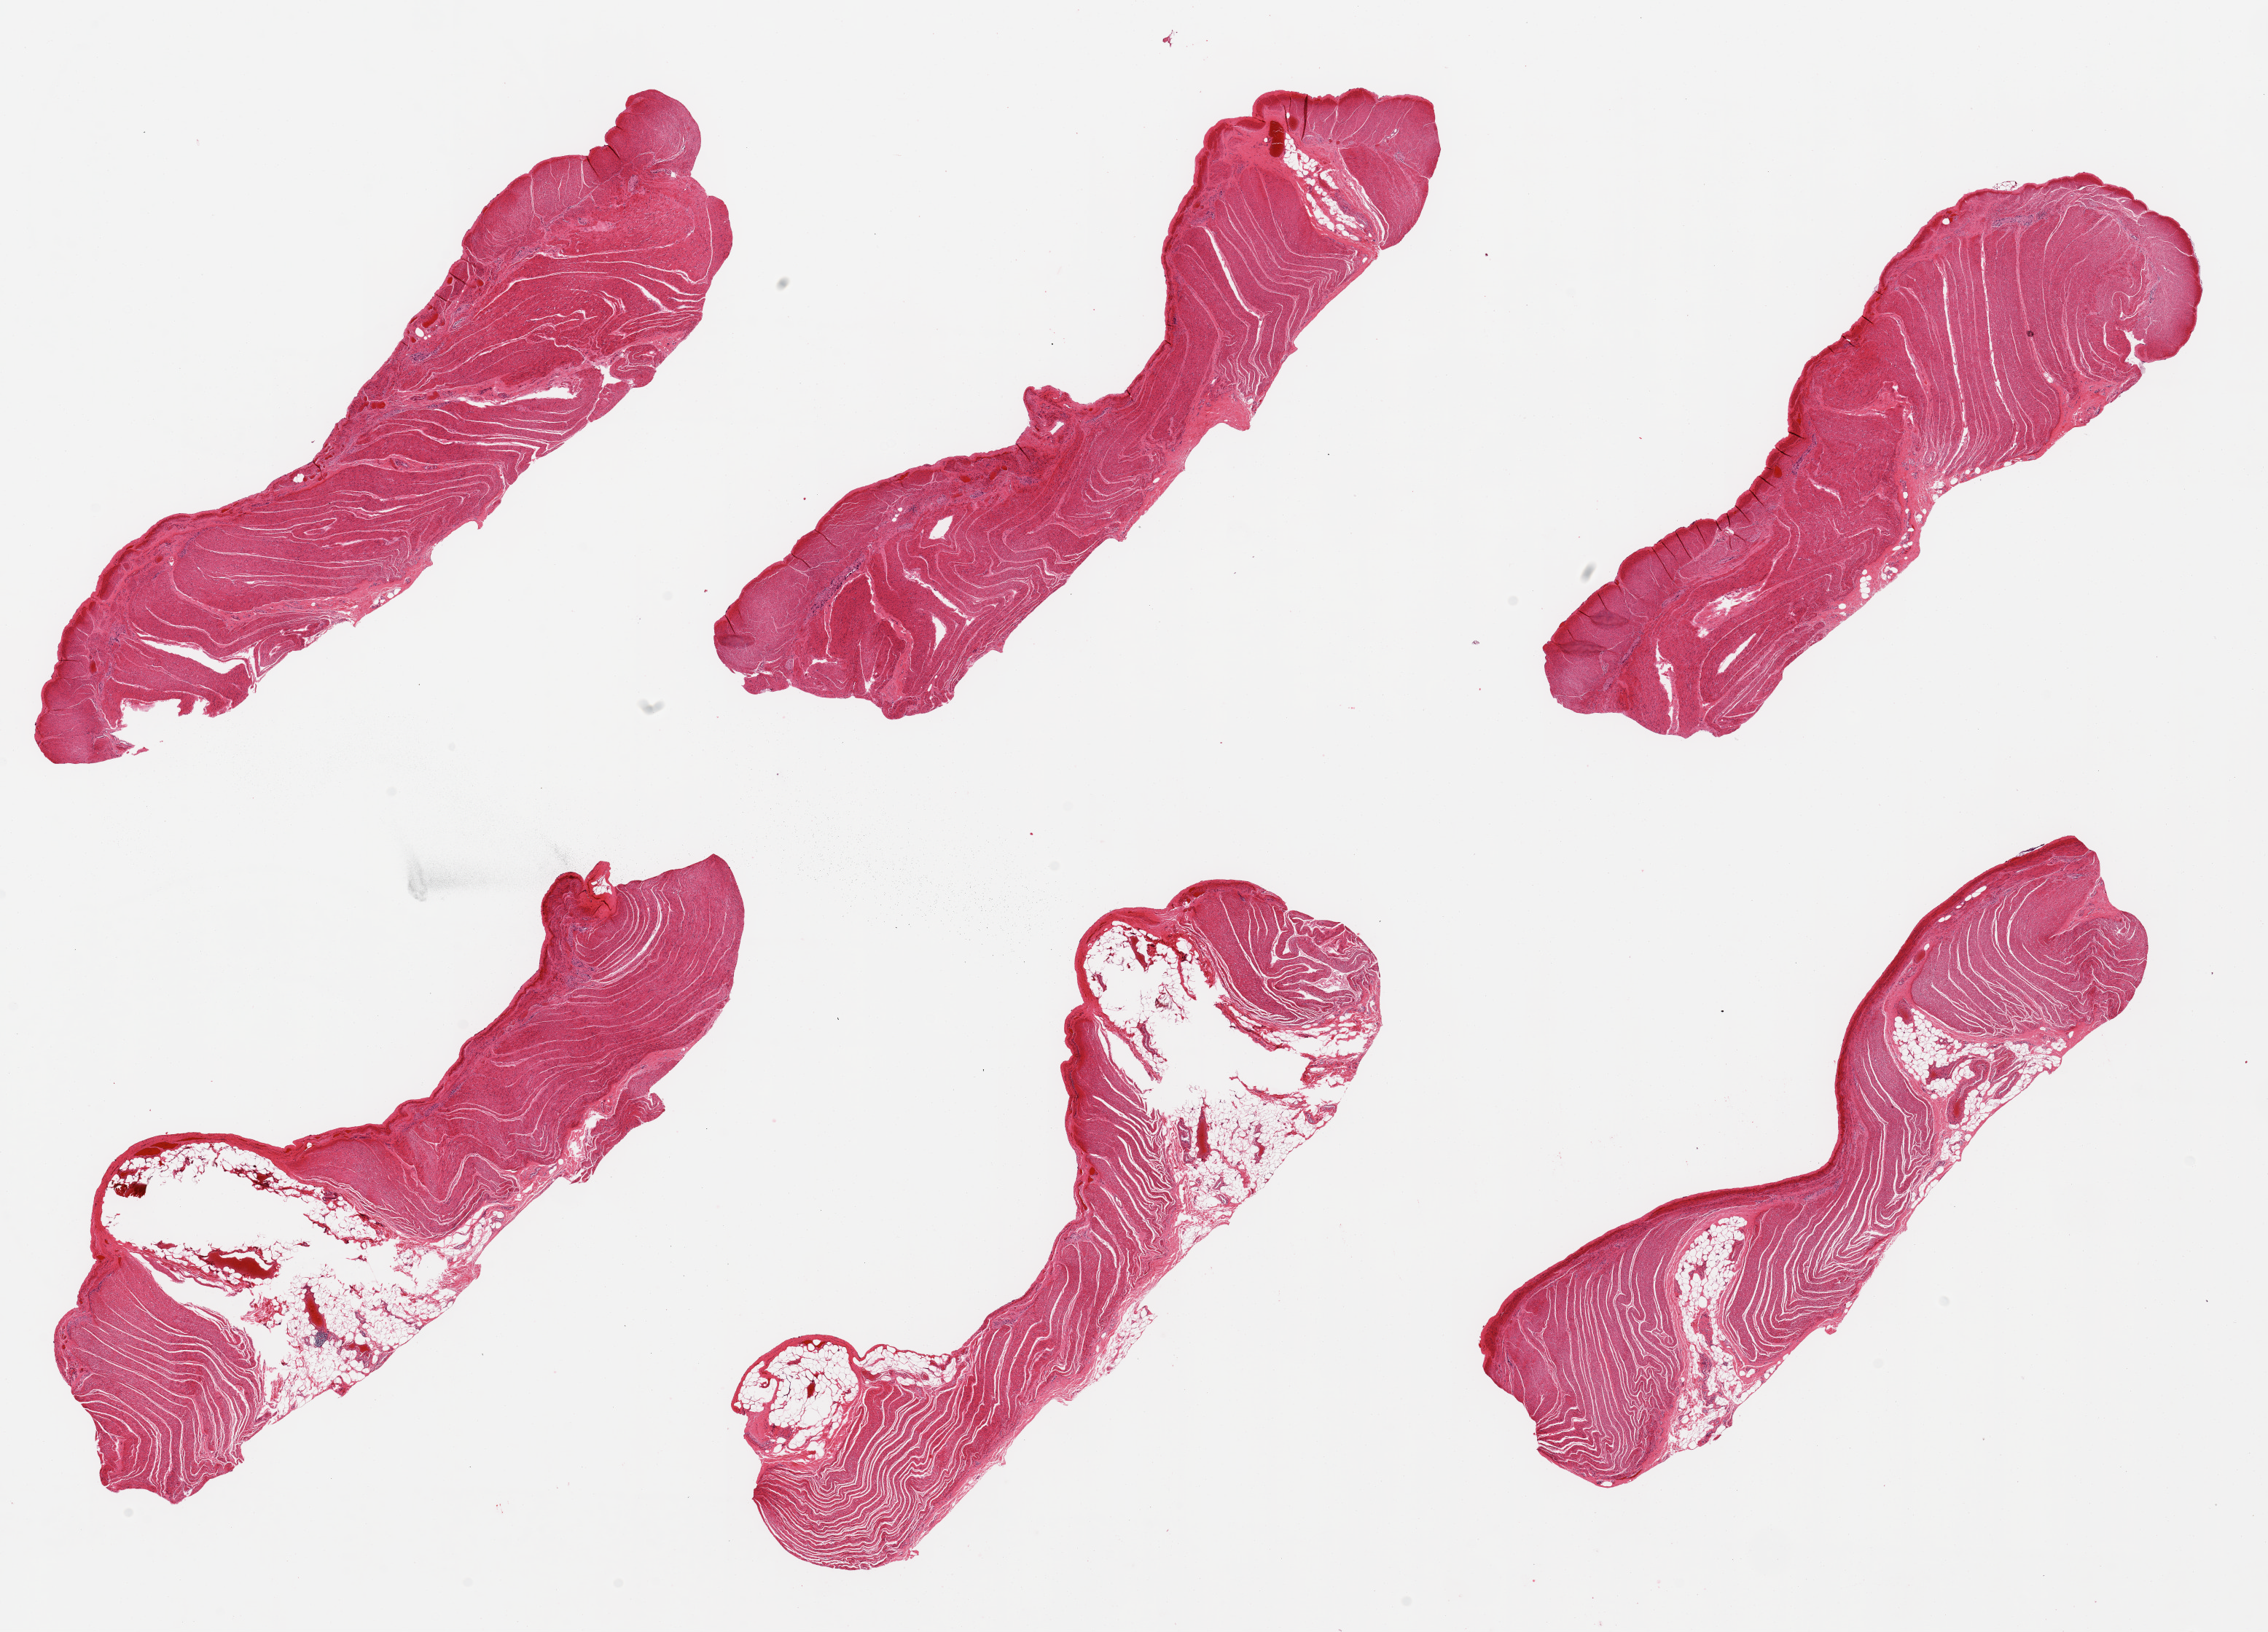
Digitized haematoxylin and eosin-stained section — whole scanned area (about 24.6 x 17.7 mm, from a 20x scan) shown as a low-resolution overview, PAXgene-fixed, paraffin-embedded tissue, target tissue: sigmoid colon, tissue donor sample. Donor: male.
Reviewer comment on this tissue sample: 6 pieces; muscularis, some fat and vessels.